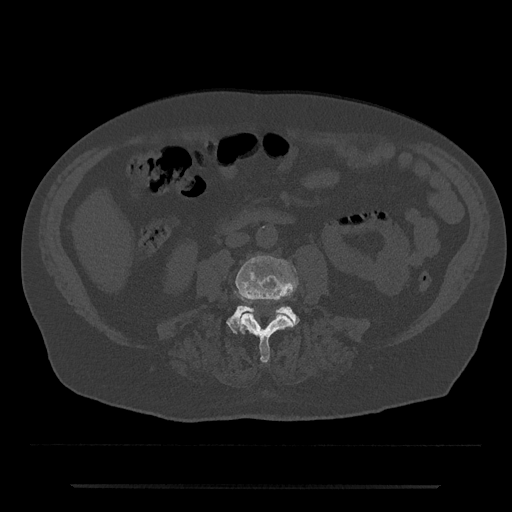
CT including the spine, one axial slice. Position 386 of 797 along the scan axis. Reconstruction kernel Br40s/3. 120 kVp. Bone window (W 1800 / L 400 HU). 512 × 512 image matrix, field of view 434 × 434 mm. Patient: male, 80 years. Case-level facts recorded for this patient, not image findings: primary cancer: prostate; vertebrae with lytic lesions (as recorded): L1, T11.
Outlined on this slice (semi-automatically segmented with operator editing):
- L3 vertebra: bounding box <236,256,298,363> (left, top, right, bottom; pixels)
- L4 vertebra: <227,305,299,333>